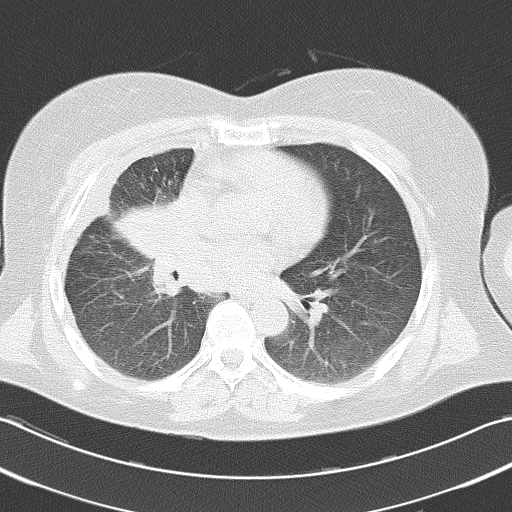
Chest CT, one axial slice. Position 16 of 38 along the scan axis. Reconstruction kernel B70f. Lung window (W 1500 / L -600 HU). 512 × 512 image matrix, field of view 346 × 346 mm. Female patient, age 52 years. From the clinical record (not read from this slice): clinical TNM (as recorded): T3 N1 M0.
Structures marked on this image (bounding box drawn by a radiologist):
- lung tumour (recorded histology: squamous cell carcinoma): bounding box [x1, y1, x2, y2] px = [109, 196, 190, 298]